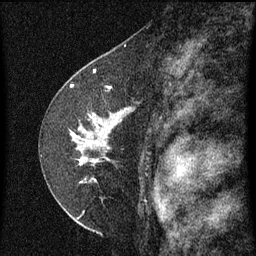
Breast MRI (dynamic contrast-enhanced), one sagittal slice; slice 41 of 60 in the series (ordered by position); dynamic contrast-enhanced series, image 2 of 3 at this slice position (ordered by acquisition); 1.5 T; TE 4.2 ms, TR 8 ms; 2 mm slice thickness; 256 × 256 image matrix. Female patient, age 47 years.
Annotated regions visible in this slice (semi-automatic segmentation, software-assisted and operator-edited):
- analysis volume of interest (the breast-tissue region the enhancement analysis was run in; not a lesion): bounding box (x1, y1, x2, y2) in pixels: (46, 84, 141, 199)
- tumour enhancement mask (voxels above the 70 % enhancement threshold inside the analysis volume of interest): (72, 84, 127, 129)